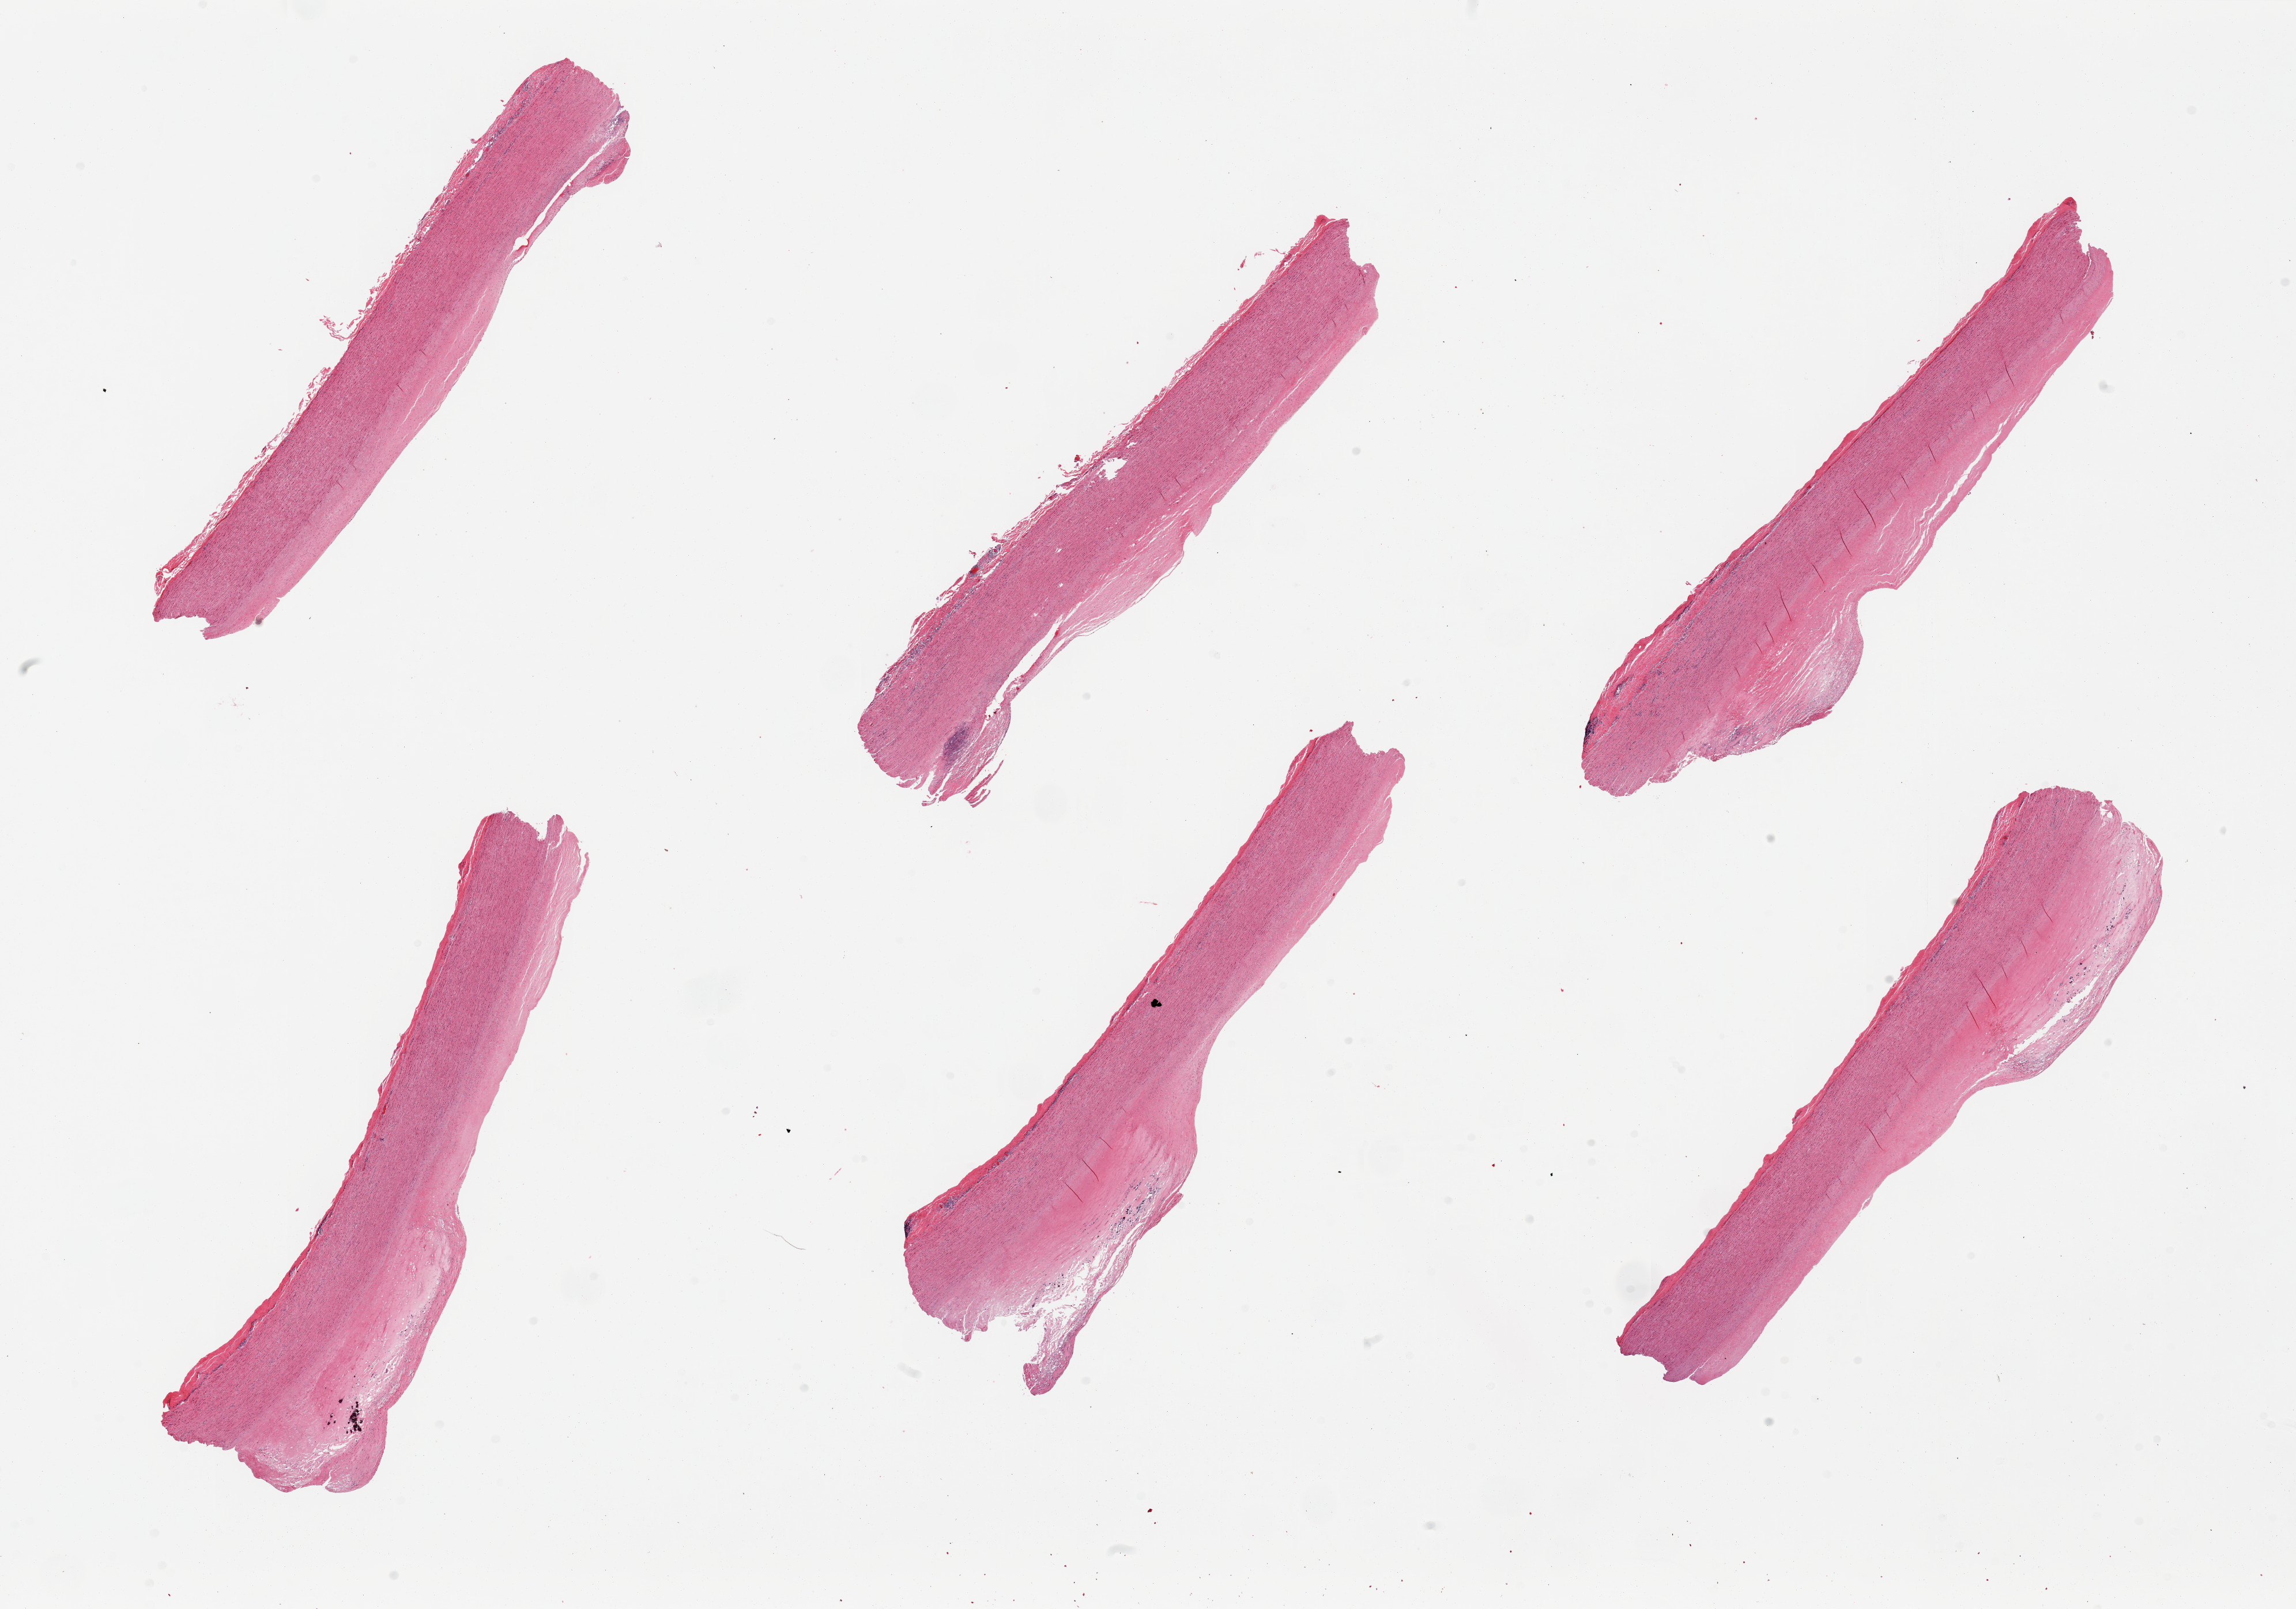
Whole-slide image, haematoxylin and eosin stain — low-resolution overview of the scanned area, about 31.5 x 22.1 mm. PAXgene-fixed, paraffin-embedded tissue. Sampled site (target tissue): aorta. Donor tissue sample. Donor sex: male.
Pathologist's review note for this sample: 6 pieces, atherosis up to ~1.5mm.